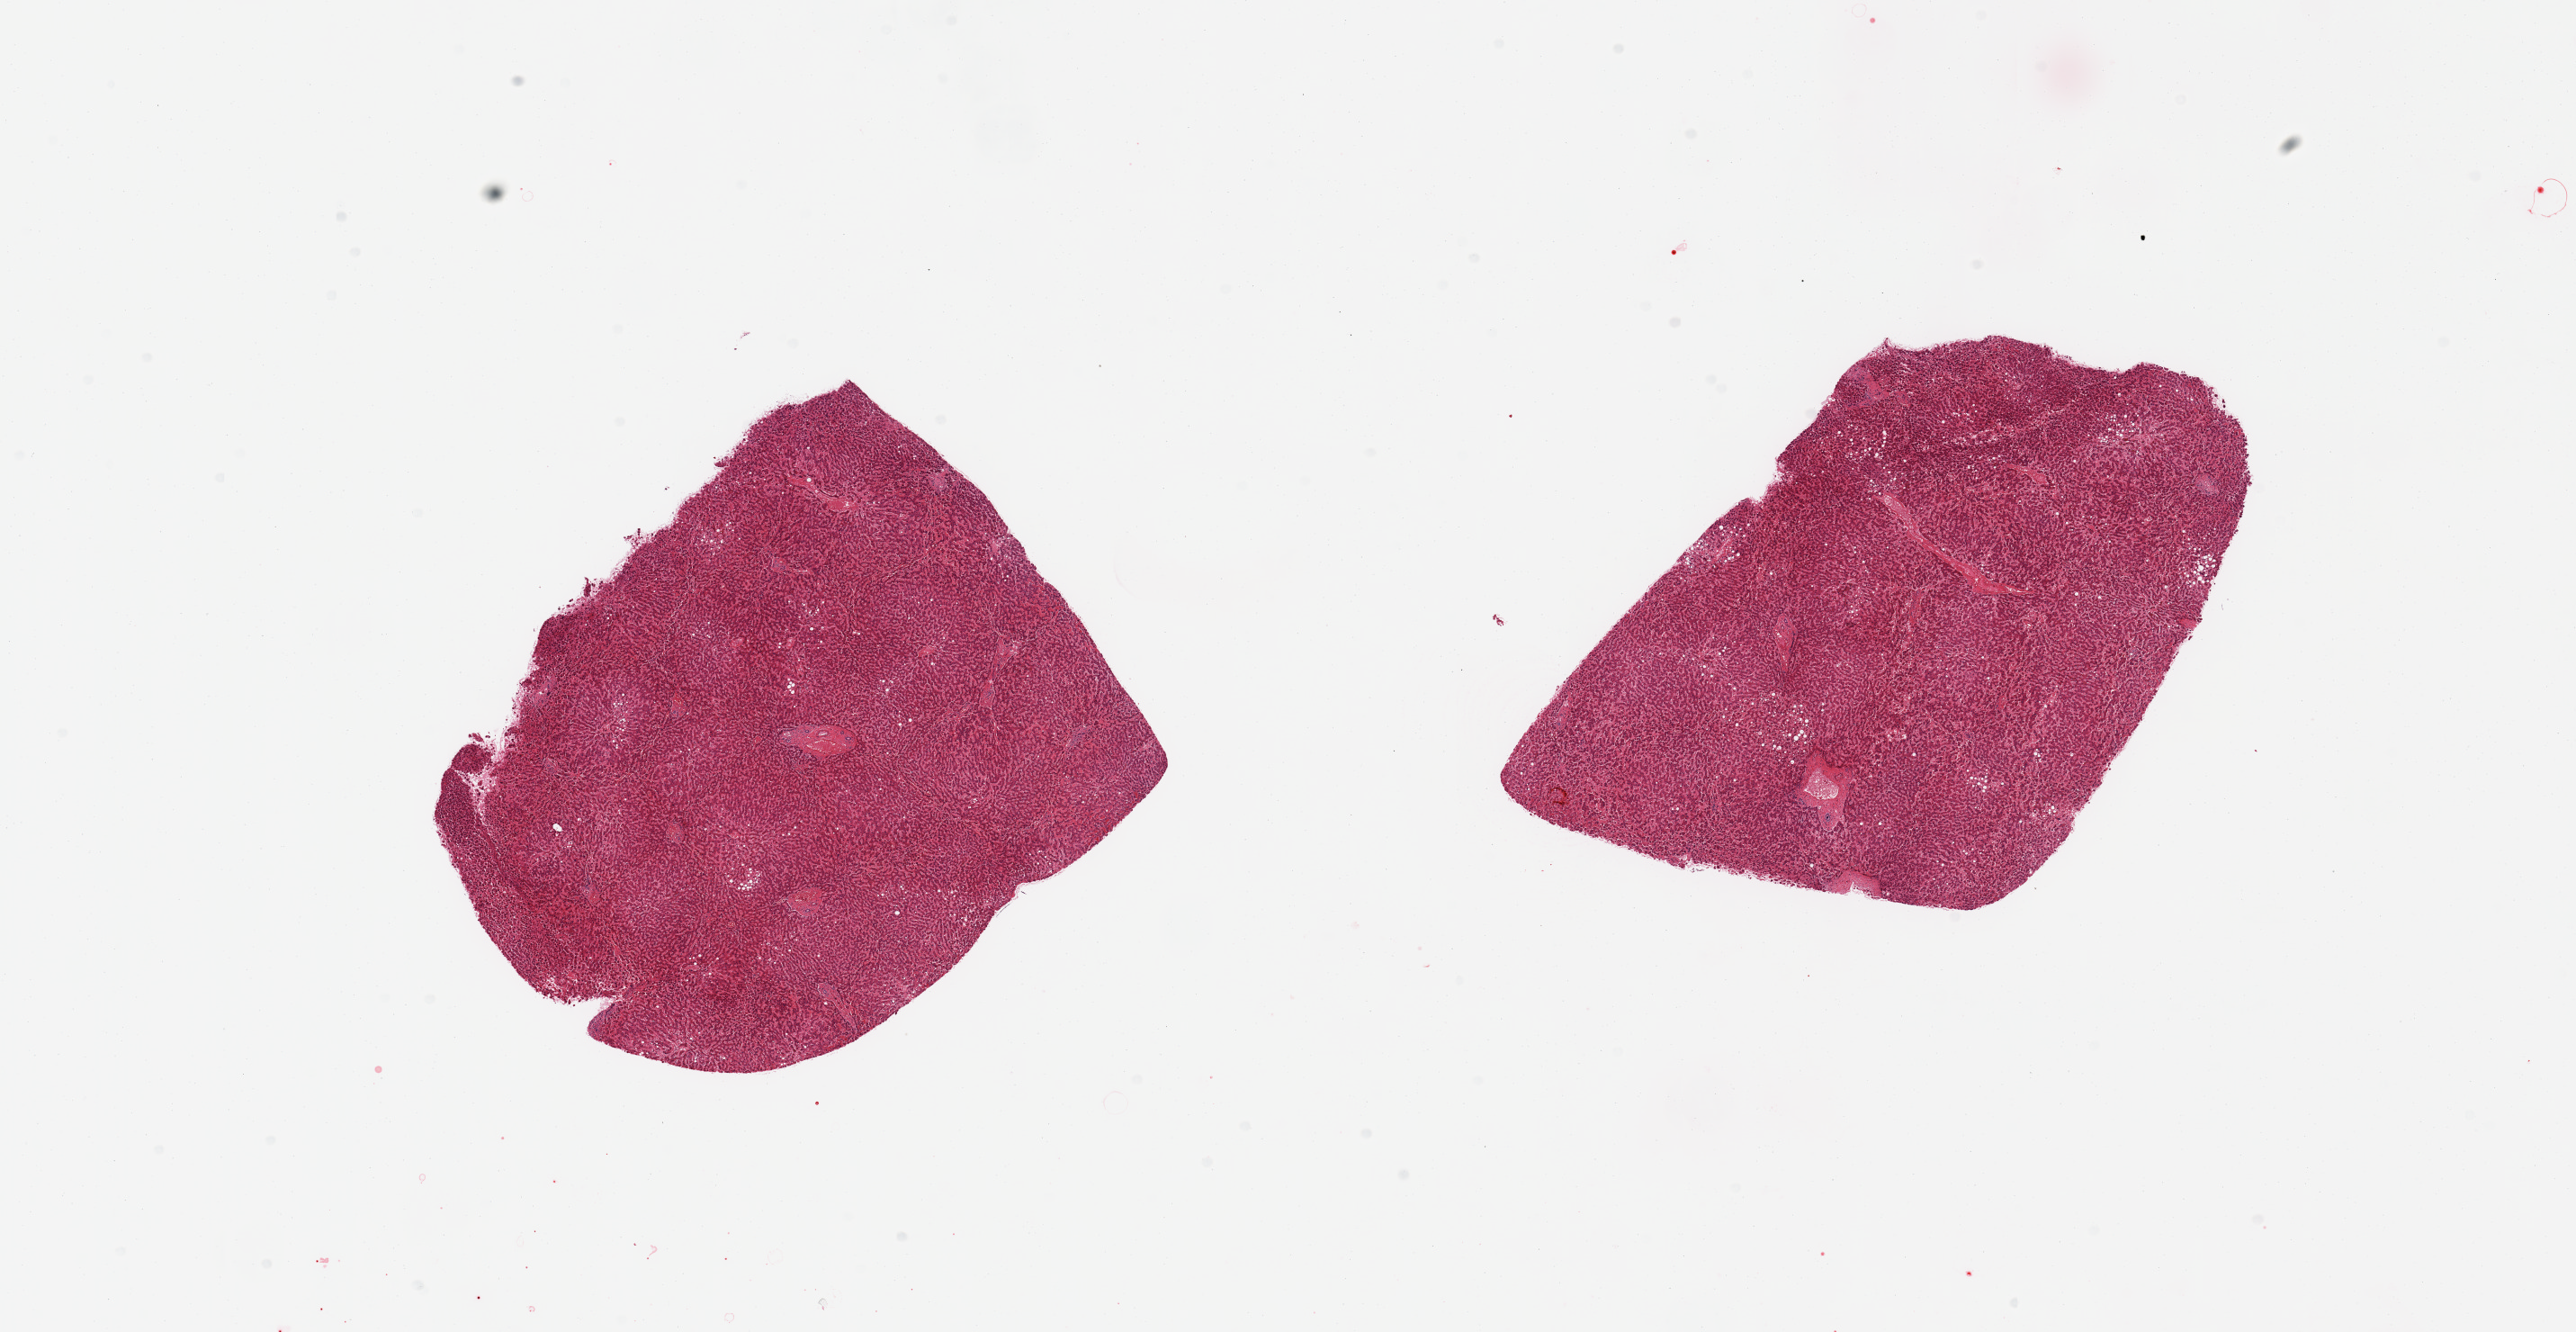
Whole-slide image, hematoxylin and eosin (H&E) stain, brightfield — whole scanned area (about 22.6 x 11.7 mm) shown as a low-resolution overview; PAXgene-fixed, paraffin-embedded tissue; target tissue: liver; tissue donor sample.
Review note (as recorded): 2 pieces, trace macrovesicular steatosis (~10% of parenchyma).